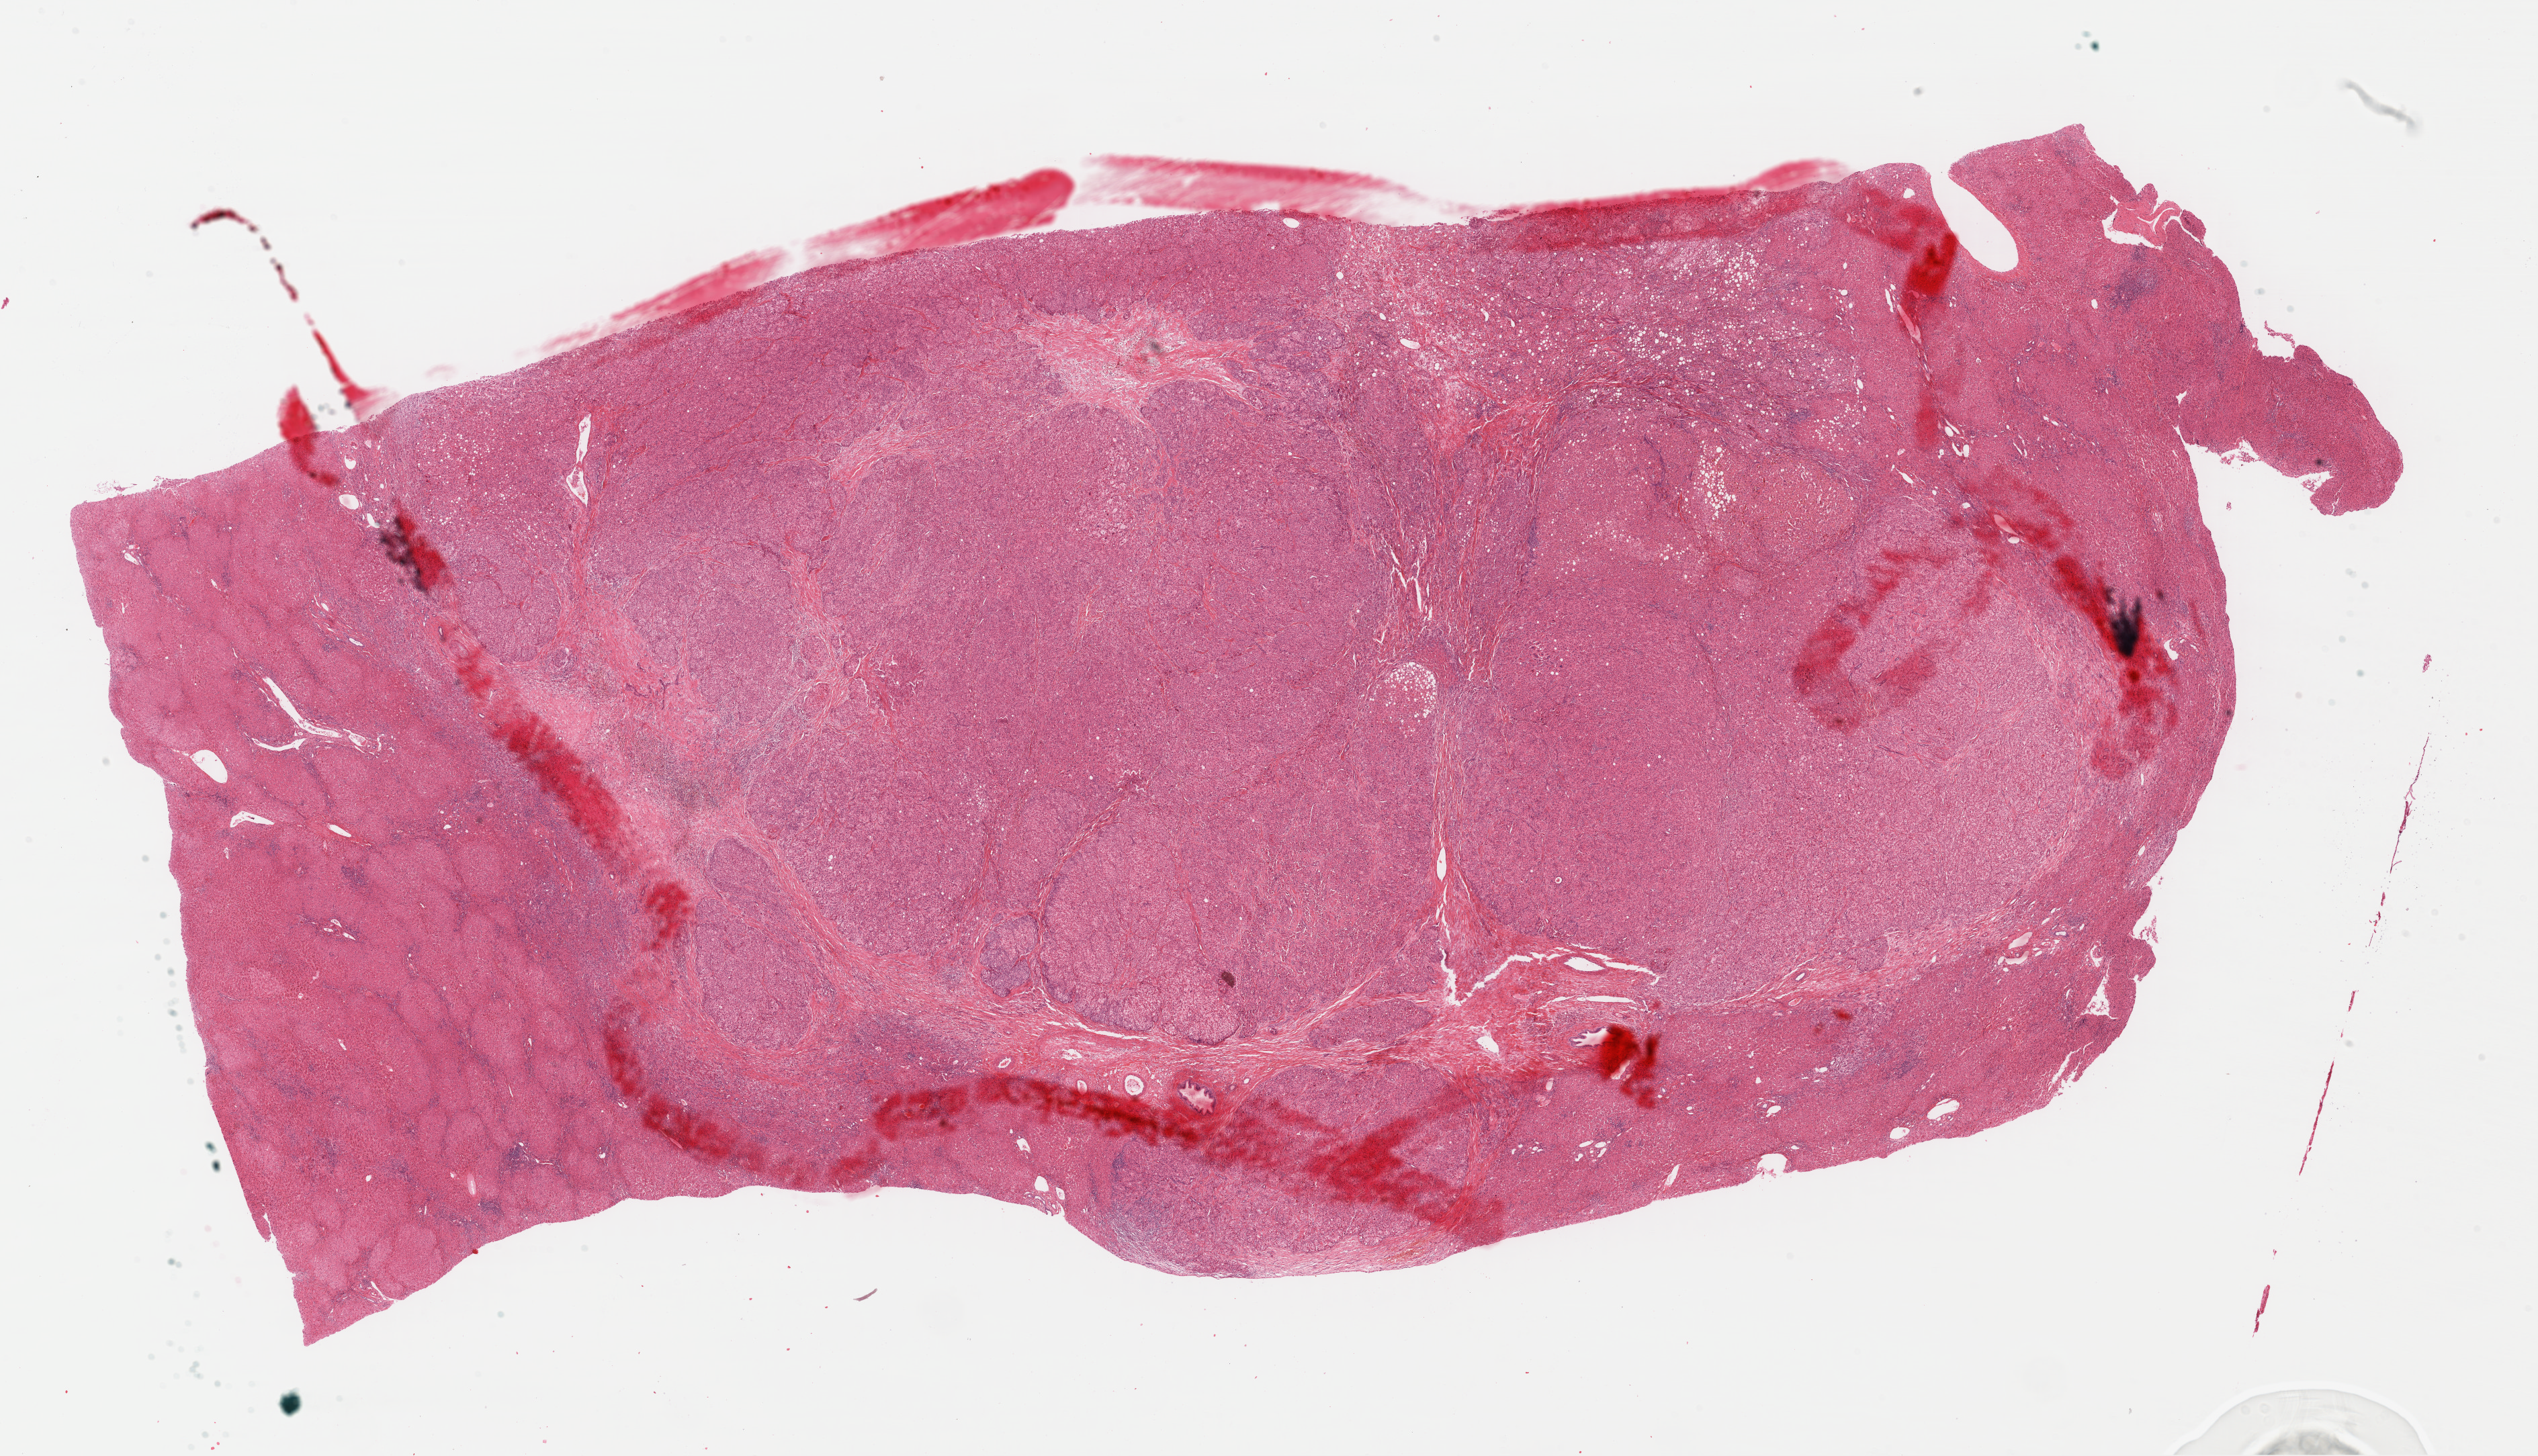
Whole-slide histology image, H&E-stained, whole scanned area (about 29.7 x 17.0 mm, acquisition: 40x scan) shown as a low-resolution overview, FFPE section, liver, primary tumour sample. Patient: male, age at initial diagnosis 58 years. Histologic grade: G3 (poorly differentiated).
* histologic diagnosis: Hepatocellular carcinoma, NOS
* AJCC pathologic stage: II (7th edition)